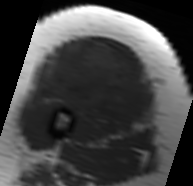
MRI of an extremity soft-tissue mass, one axial slice. Slice 34 of 91 in the series (ordered by position). MR volume resampled by the dataset authors to the PET/CT grid (not the native acquisition matrix). 3.27 mm slice thickness. 193 × 186 image matrix. Female patient. From the clinical record (not read from this slice): histological type: malignant solitary fibrous tumor; grade: intermediate; site of the primary tumour: right thigh.
Outlined on this slice (expert contour drawn on MRI and transferred to this co-registered scan by the dataset authors):
- gross tumour volume including surrounding oedema: bounding box <31,39,150,132> (left, top, right, bottom; pixels)
- gross tumour volume (mass): <38,39,148,127>